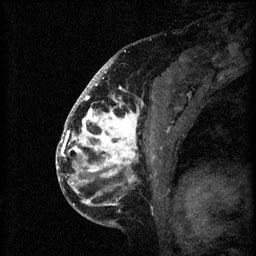
Breast MRI (dynamic contrast-enhanced), one sagittal slice; position 36 of 60 along the scan axis; 3 images stored at this slice position (order not interpretable as contrast timing); 1.5 T; TE 4.2 ms, TR 8.2 ms; 2 mm slice thickness; 256 × 256 image matrix. Patient: female, 41 years.
Outlined on this slice (semi-automatically segmented with operator editing):
- analysis volume of interest (the breast-tissue region the enhancement analysis was run in; not a lesion): bounding box (x1, y1, x2, y2) in pixels: (72, 108, 162, 205)
- tumour enhancement mask (voxels above the 70 % enhancement threshold inside the analysis volume of interest): (72, 108, 139, 205)